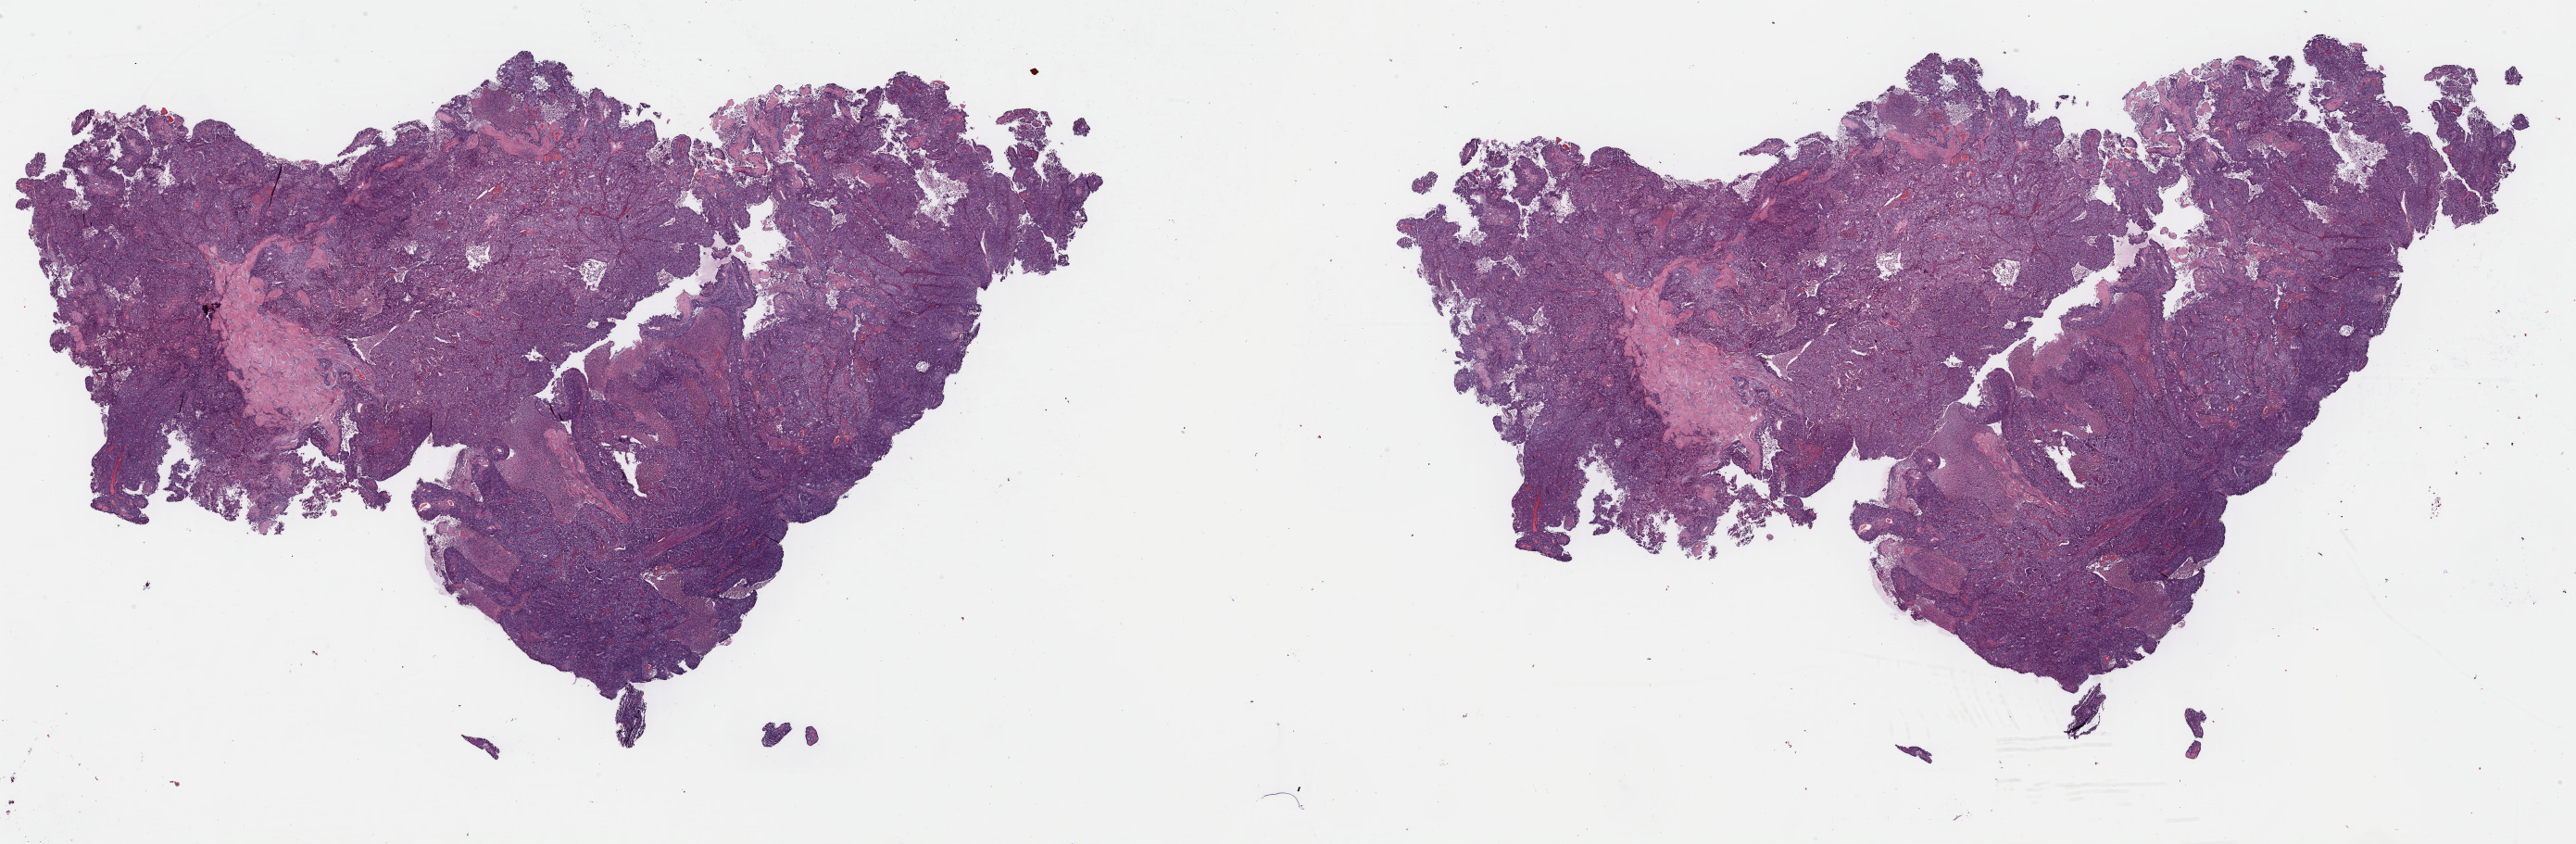
Whole-slide histology image, Hematoxylin and eosin (H&E) stained, low-resolution overview of the scanned area, about 43.9 x 14.4 mm; formalin-fixed paraffin-embedded (FFPE) diagnostic section; sample: primary tumour, uterus. Female patient; age at initial diagnosis 74 years.
Diagnosis: Endometrioid adenocarcinoma, NOS (endometrium).